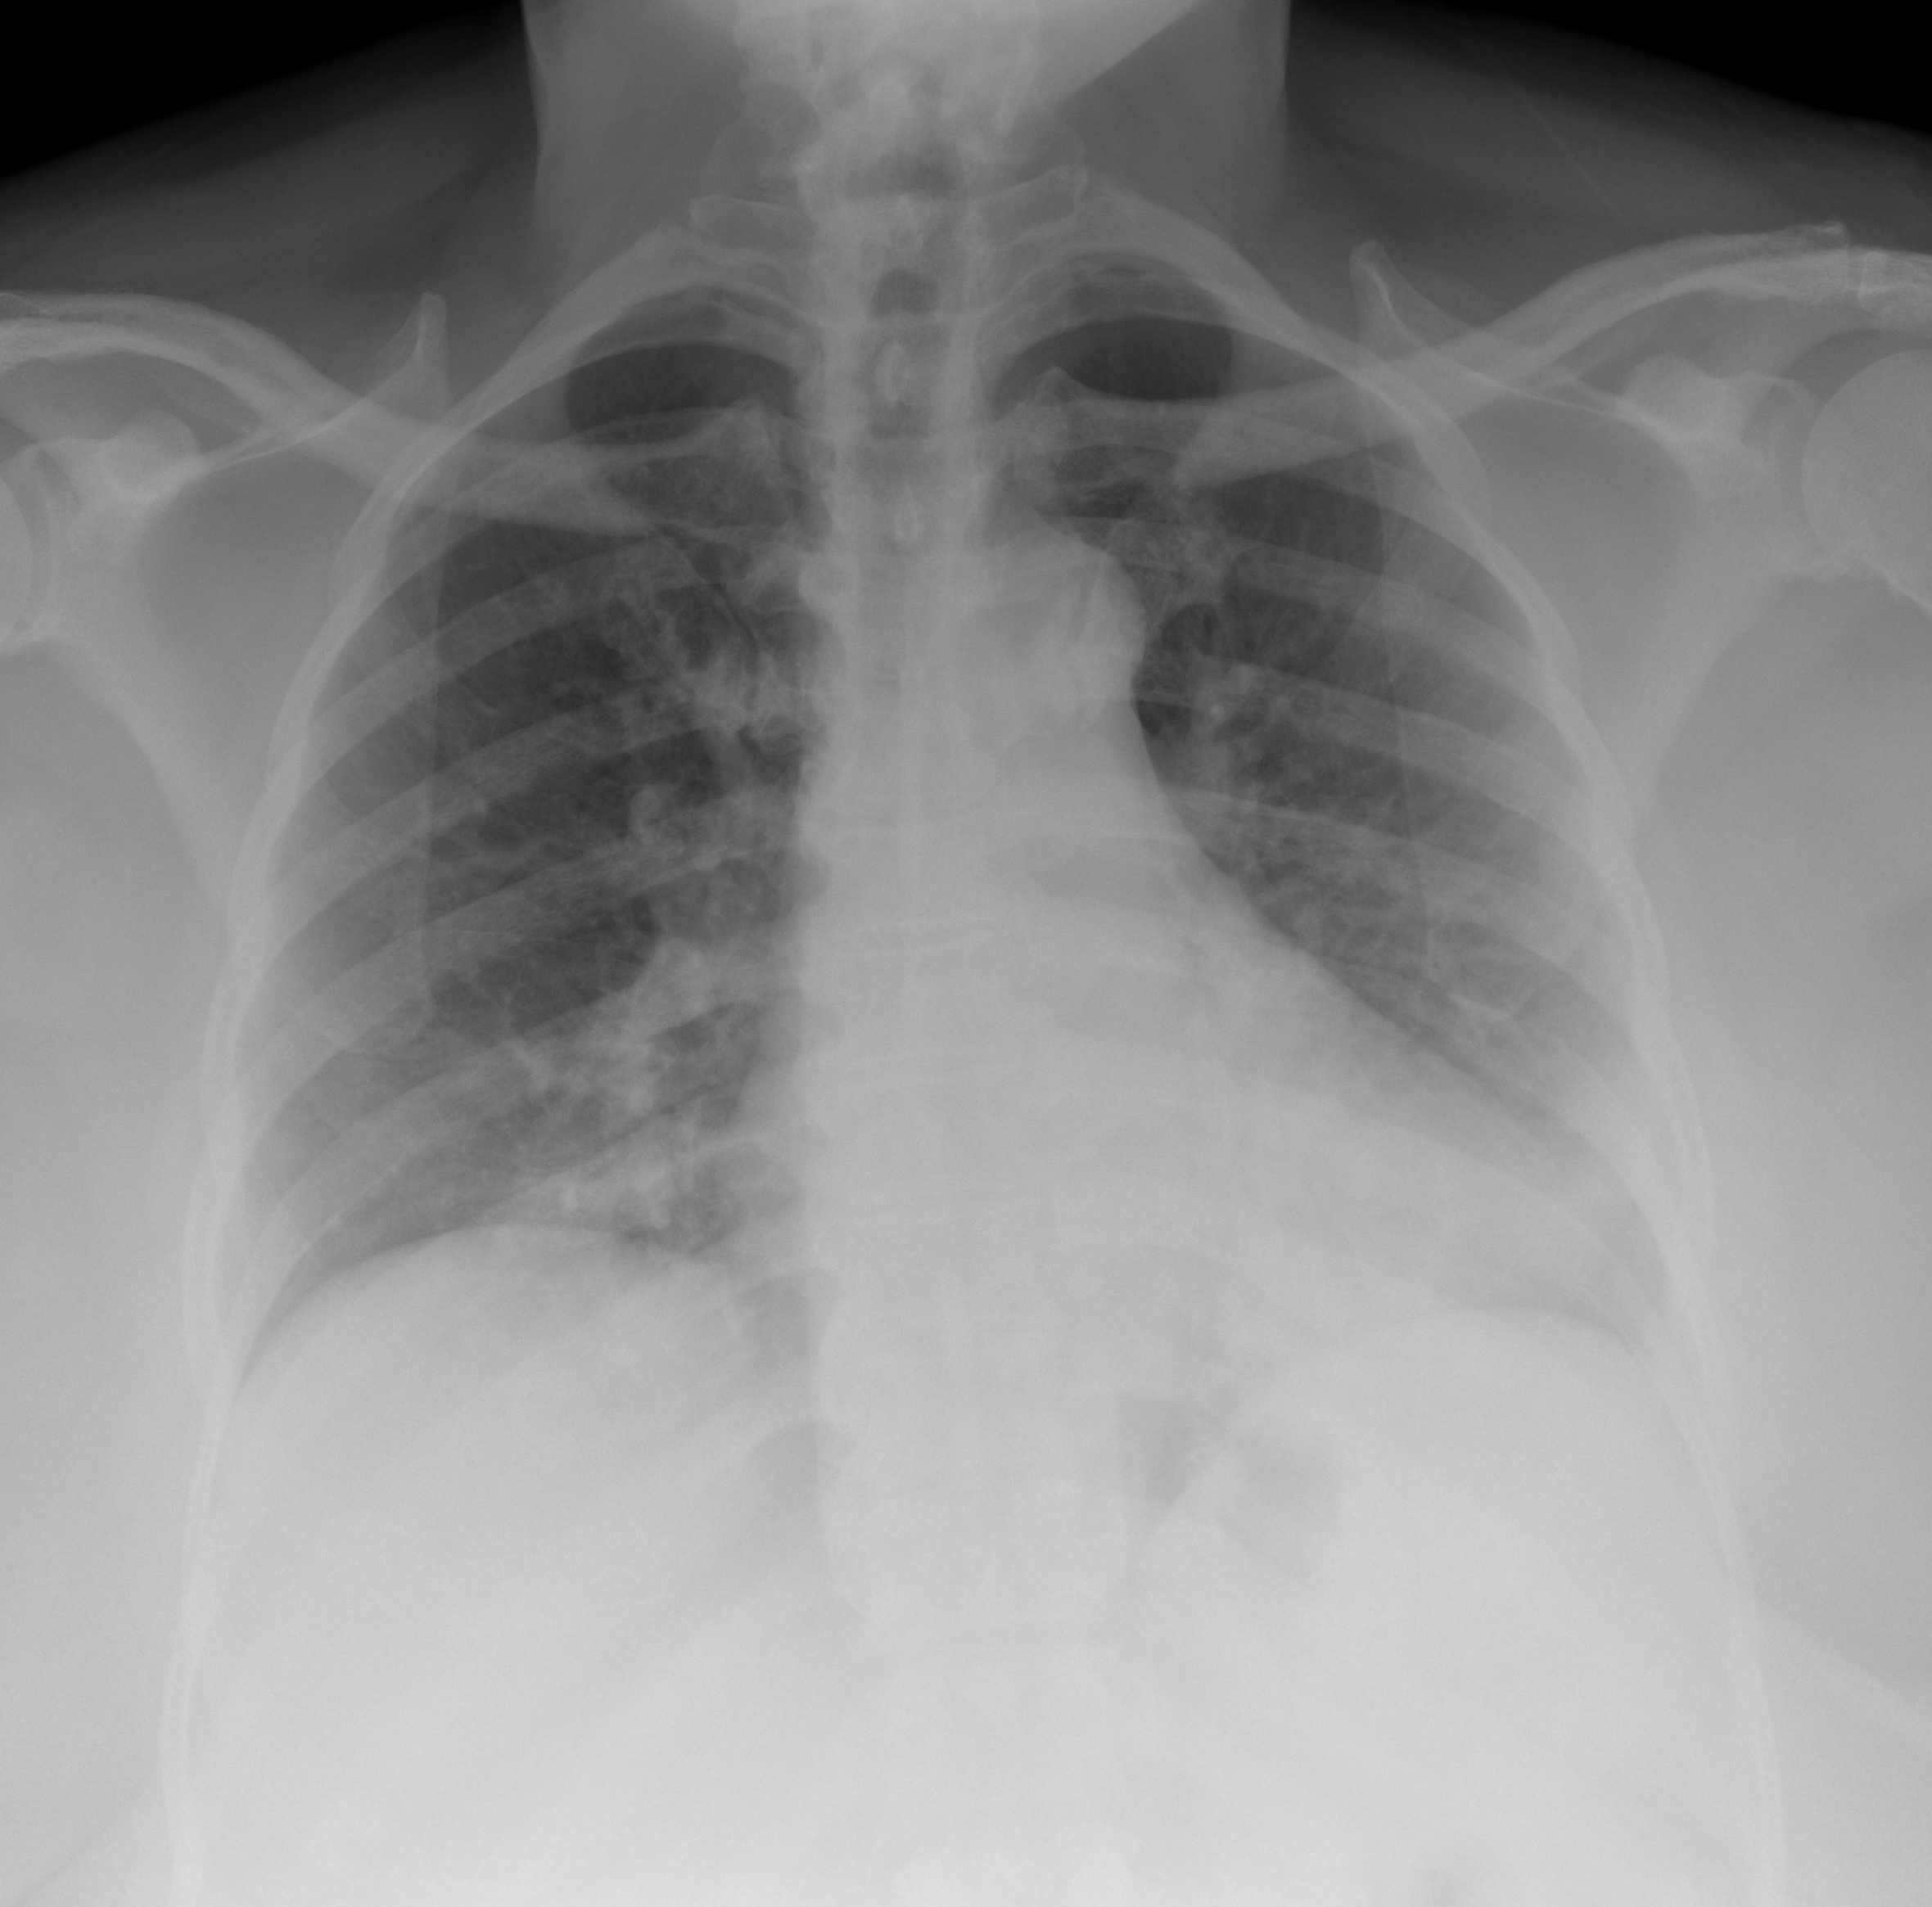
Chest X-ray (portable), AP projection. Female patient, age 61 years; imaged 4 days after the COVID-19 diagnosis.
Radiologist key findings (as recorded): Interval development of patchy areas of consolidation predominately in the lung bases suspicious for infection.